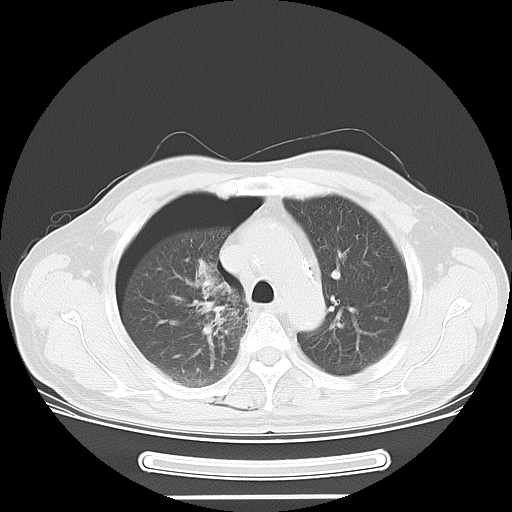
Chest CT, one axial slice; slice 42 of 57 in the series (ordered by position); 120 kVp; lung window (W 1500 / L -600 HU); 5 mm slice thickness; 512 × 512 image matrix, field of view 376 × 376 mm. Male patient, age 61 years. Case-level facts recorded for this patient, not image findings: clinical TNM (as recorded): T1c N3 M1b.
Annotated regions visible in this slice (bounding box drawn by a radiologist):
- lung tumour (recorded histology: adenocarcinoma): bounding box <174,258,256,371> (left, top, right, bottom; pixels)